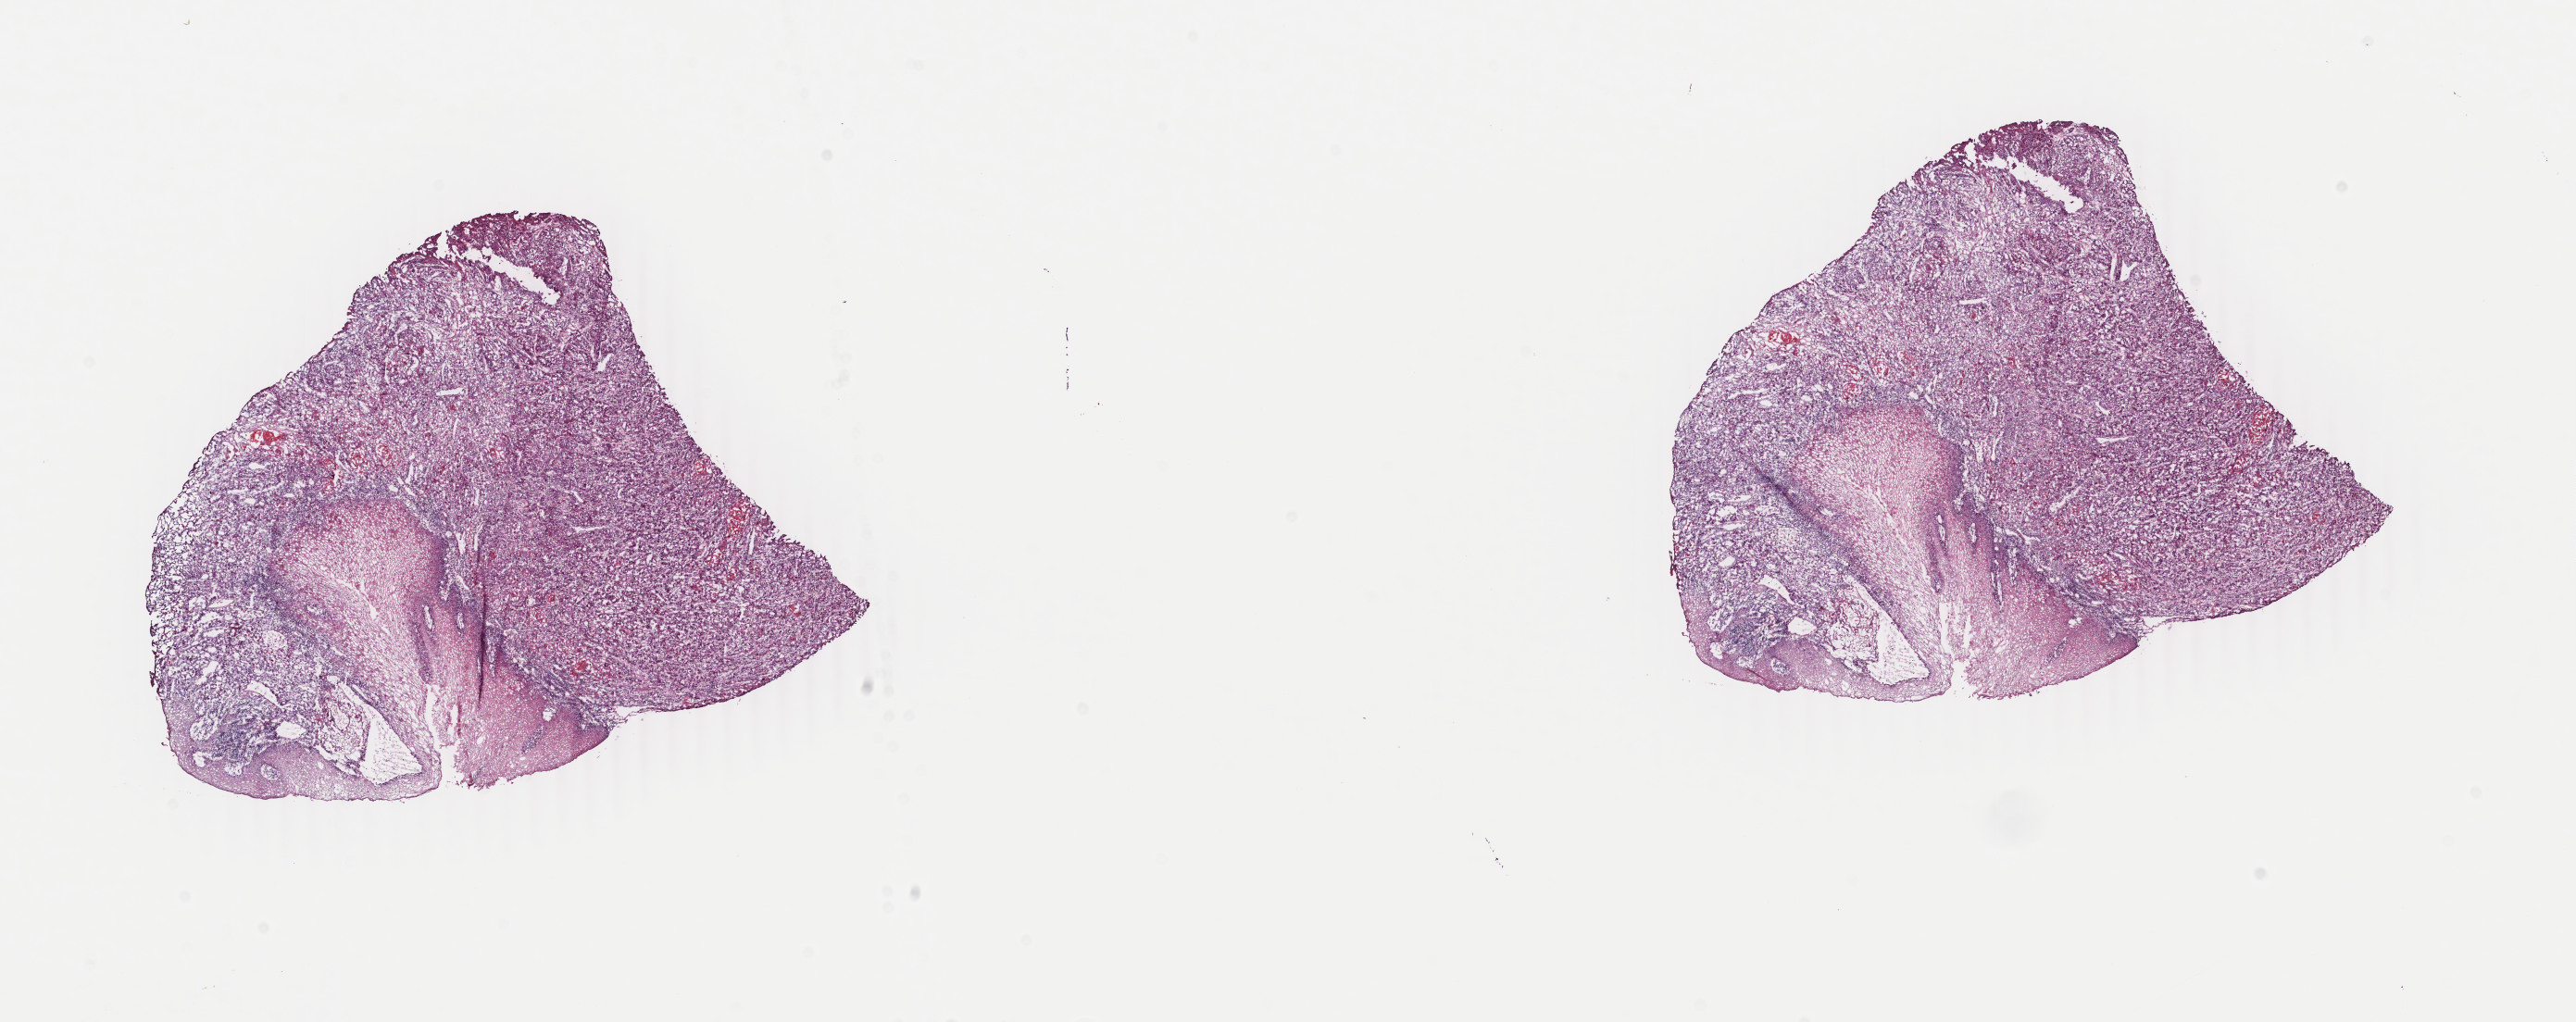
Digitized H&E tissue section (whole slide) — low-resolution overview of the scanned area, about 22.1 x 8.8 mm (acquisition: 40x scan). Frozen section from the top of the tissue portion. Esophagus, primary tumour sample. Patient: female, age at initial diagnosis 51 years. Histologic grade: G1 (well differentiated). Pathologist review of this section (percent, as recorded): tumour cells 90%, tumour nuclei 85%, normal cells 0%, stromal cells 10%, necrosis 0%. Infiltration values recorded for this section: lymphocyte infiltration 6%, monocyte infiltration 2%, neutrophil infiltration 0%.
Lymph nodes positive (case pathology): 0 of 26 examined. AJCC pathologic stage: IIA (6th edition). TNM: T3 N0 M0. Diagnosis: Squamous cell carcinoma, NOS (lower third of esophagus).